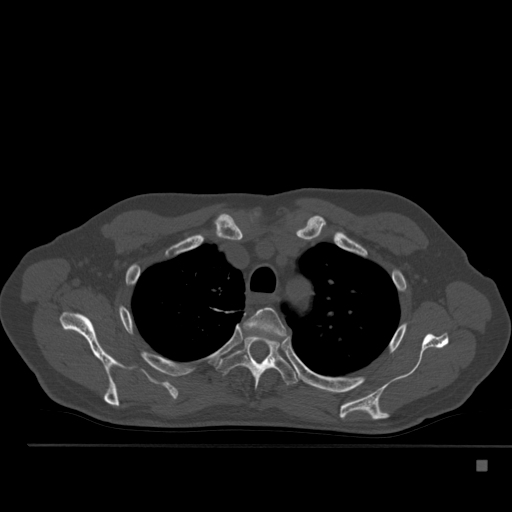
CT including the spine, one axial slice. Slice 387 of 517 in the series (ordered by position). Reconstruction kernel Br40s. 120 kVp. Bone window (W 1800 / L 400 HU). 1.5 mm slice thickness. 512 × 512 image matrix. Patient: male, 70 years. Case-level facts recorded for this patient, not image findings: primary cancer: renal; vertebrae with lytic lesions (as recorded): T4, T6, T10, T12, L3, L4, L5.
Structures marked on this image (semi-automatically segmented with operator editing):
- T3 vertebra: bounding box (x1, y1, x2, y2) in pixels: (242, 307, 286, 336)
- T4 vertebra: (216, 335, 299, 390)